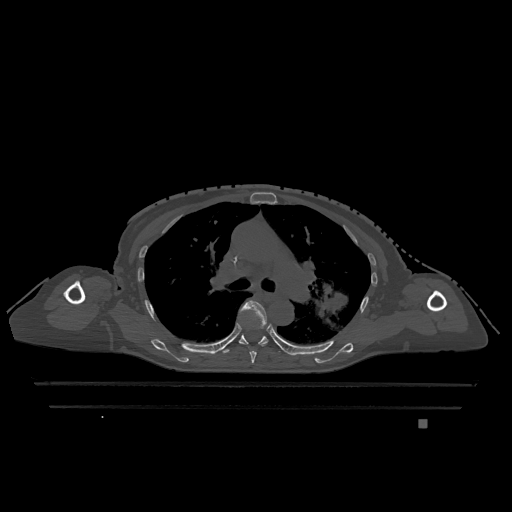
CT including the spine, one axial slice; slice 813 of 1317 in the series (ordered by position); bone window (W 1800 / L 400 HU); 0.5 mm slice thickness; 512 × 512 image matrix. Patient: female, 74 years. From the clinical record (not read from this slice): primary cancer: lung.
Structures marked on this image (semi-automatic segmentation, software-assisted and operator-edited):
- T5 vertebra: bounding box [x1, y1, x2, y2] px = [241, 301, 267, 363]
- T6 vertebra: [223, 334, 268, 354]